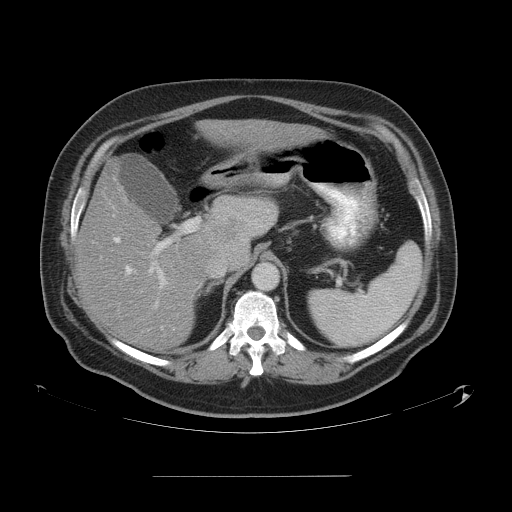
Contrast-enhanced abdominal CT, one axial slice. Position 35 of 58 along the scan axis. 120 kVp. Soft-tissue window (W 400 / L 40 HU). 5 mm slice thickness. 512 × 512 image matrix, field of view 480 × 480 mm. Male patient, age 63 years. Case-level facts recorded for this patient, not image findings: diagnosis: colorectal cancer liver metastases, imaged before liver resection; multiple liver metastases: no; largest metastasis: 4.2 cm.
Outlined on this slice (expert manual segmentation):
- hepatic veins: box from (x=113, y=206) to (x=224, y=261) px
- liver: (x=77, y=120)–(x=310, y=350)
- planned liver remnant (the part of the liver to remain after resection): (x=77, y=193)–(x=205, y=350)
- portal vein (with intrahepatic branches): (x=114, y=218)–(x=200, y=329)
- liver metastasis: (x=215, y=215)–(x=239, y=242)